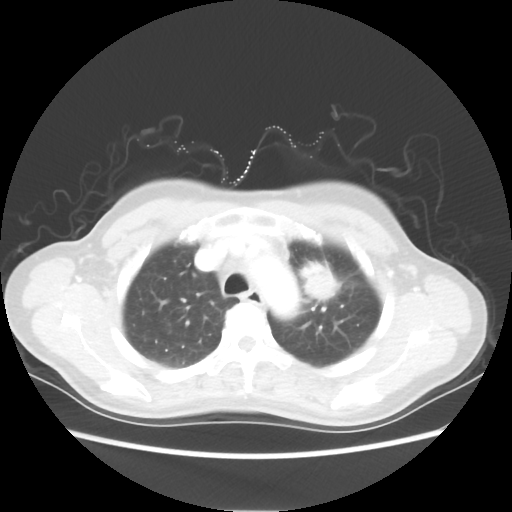
Chest CT, one axial slice. Position 42 of 54 along the scan axis. 80 kVp. Lung window (W 1500 / L -600 HU). 5 mm slice thickness. 512 × 512 image matrix, field of view 360 × 360 mm. Patient: female, 53 years. From the clinical record (not read from this slice): clinical TNM (as recorded): T1c N0 M0.
Structures marked on this image (rectangle marked by the reading radiologist):
- lung tumour (recorded histology: adenocarcinoma): box from (x=295, y=253) to (x=343, y=307) px
- lung tumour (recorded histology: adenocarcinoma): (x=301, y=261)–(x=340, y=309)